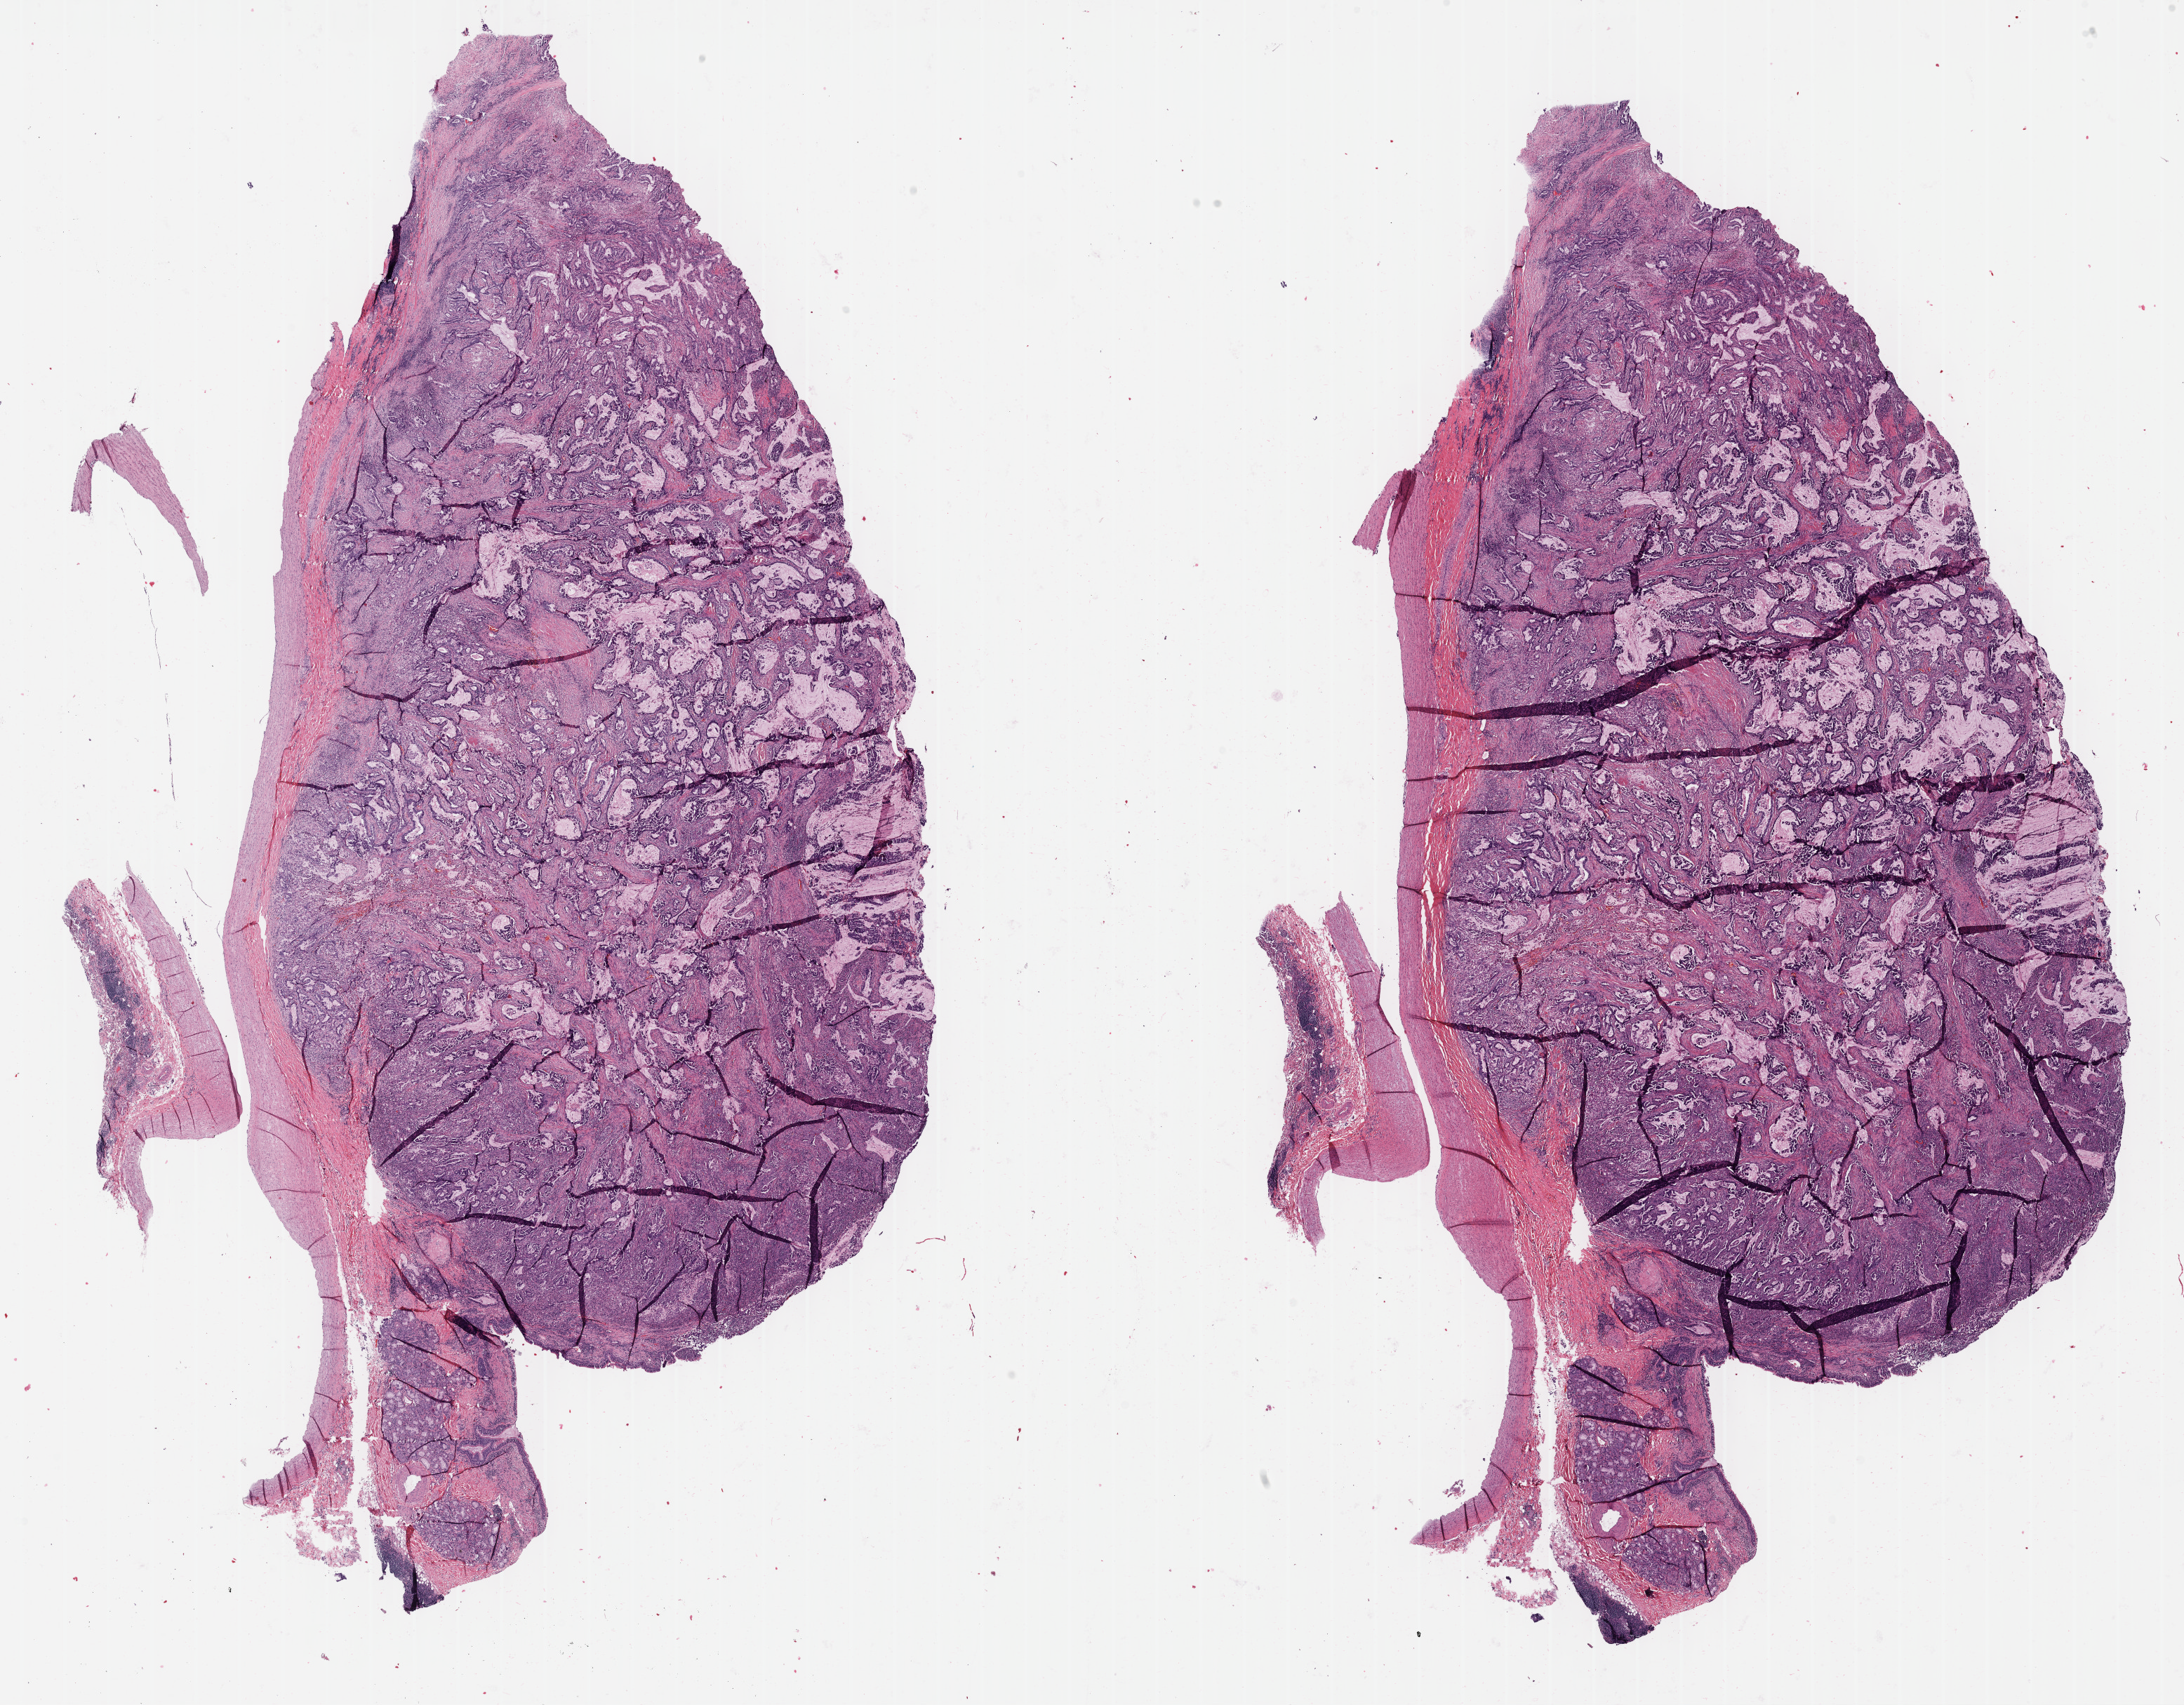
Whole-slide histology image, Hematoxylin and eosin (H&E) stained, a low-resolution overview of the entire scanned area, about 25.2 x 19.7 mm (slide scanned at 40x); formalin-fixed paraffin-embedded (FFPE) diagnostic section; sample: primary tumour, lung. Male patient; age at initial diagnosis 52 years.
AJCC pathologic stage: IB (7th edition). TNM: T2a N0 M0. Histologic diagnosis: Adenocarcinoma with mixed subtypes (lower lobe, lung).